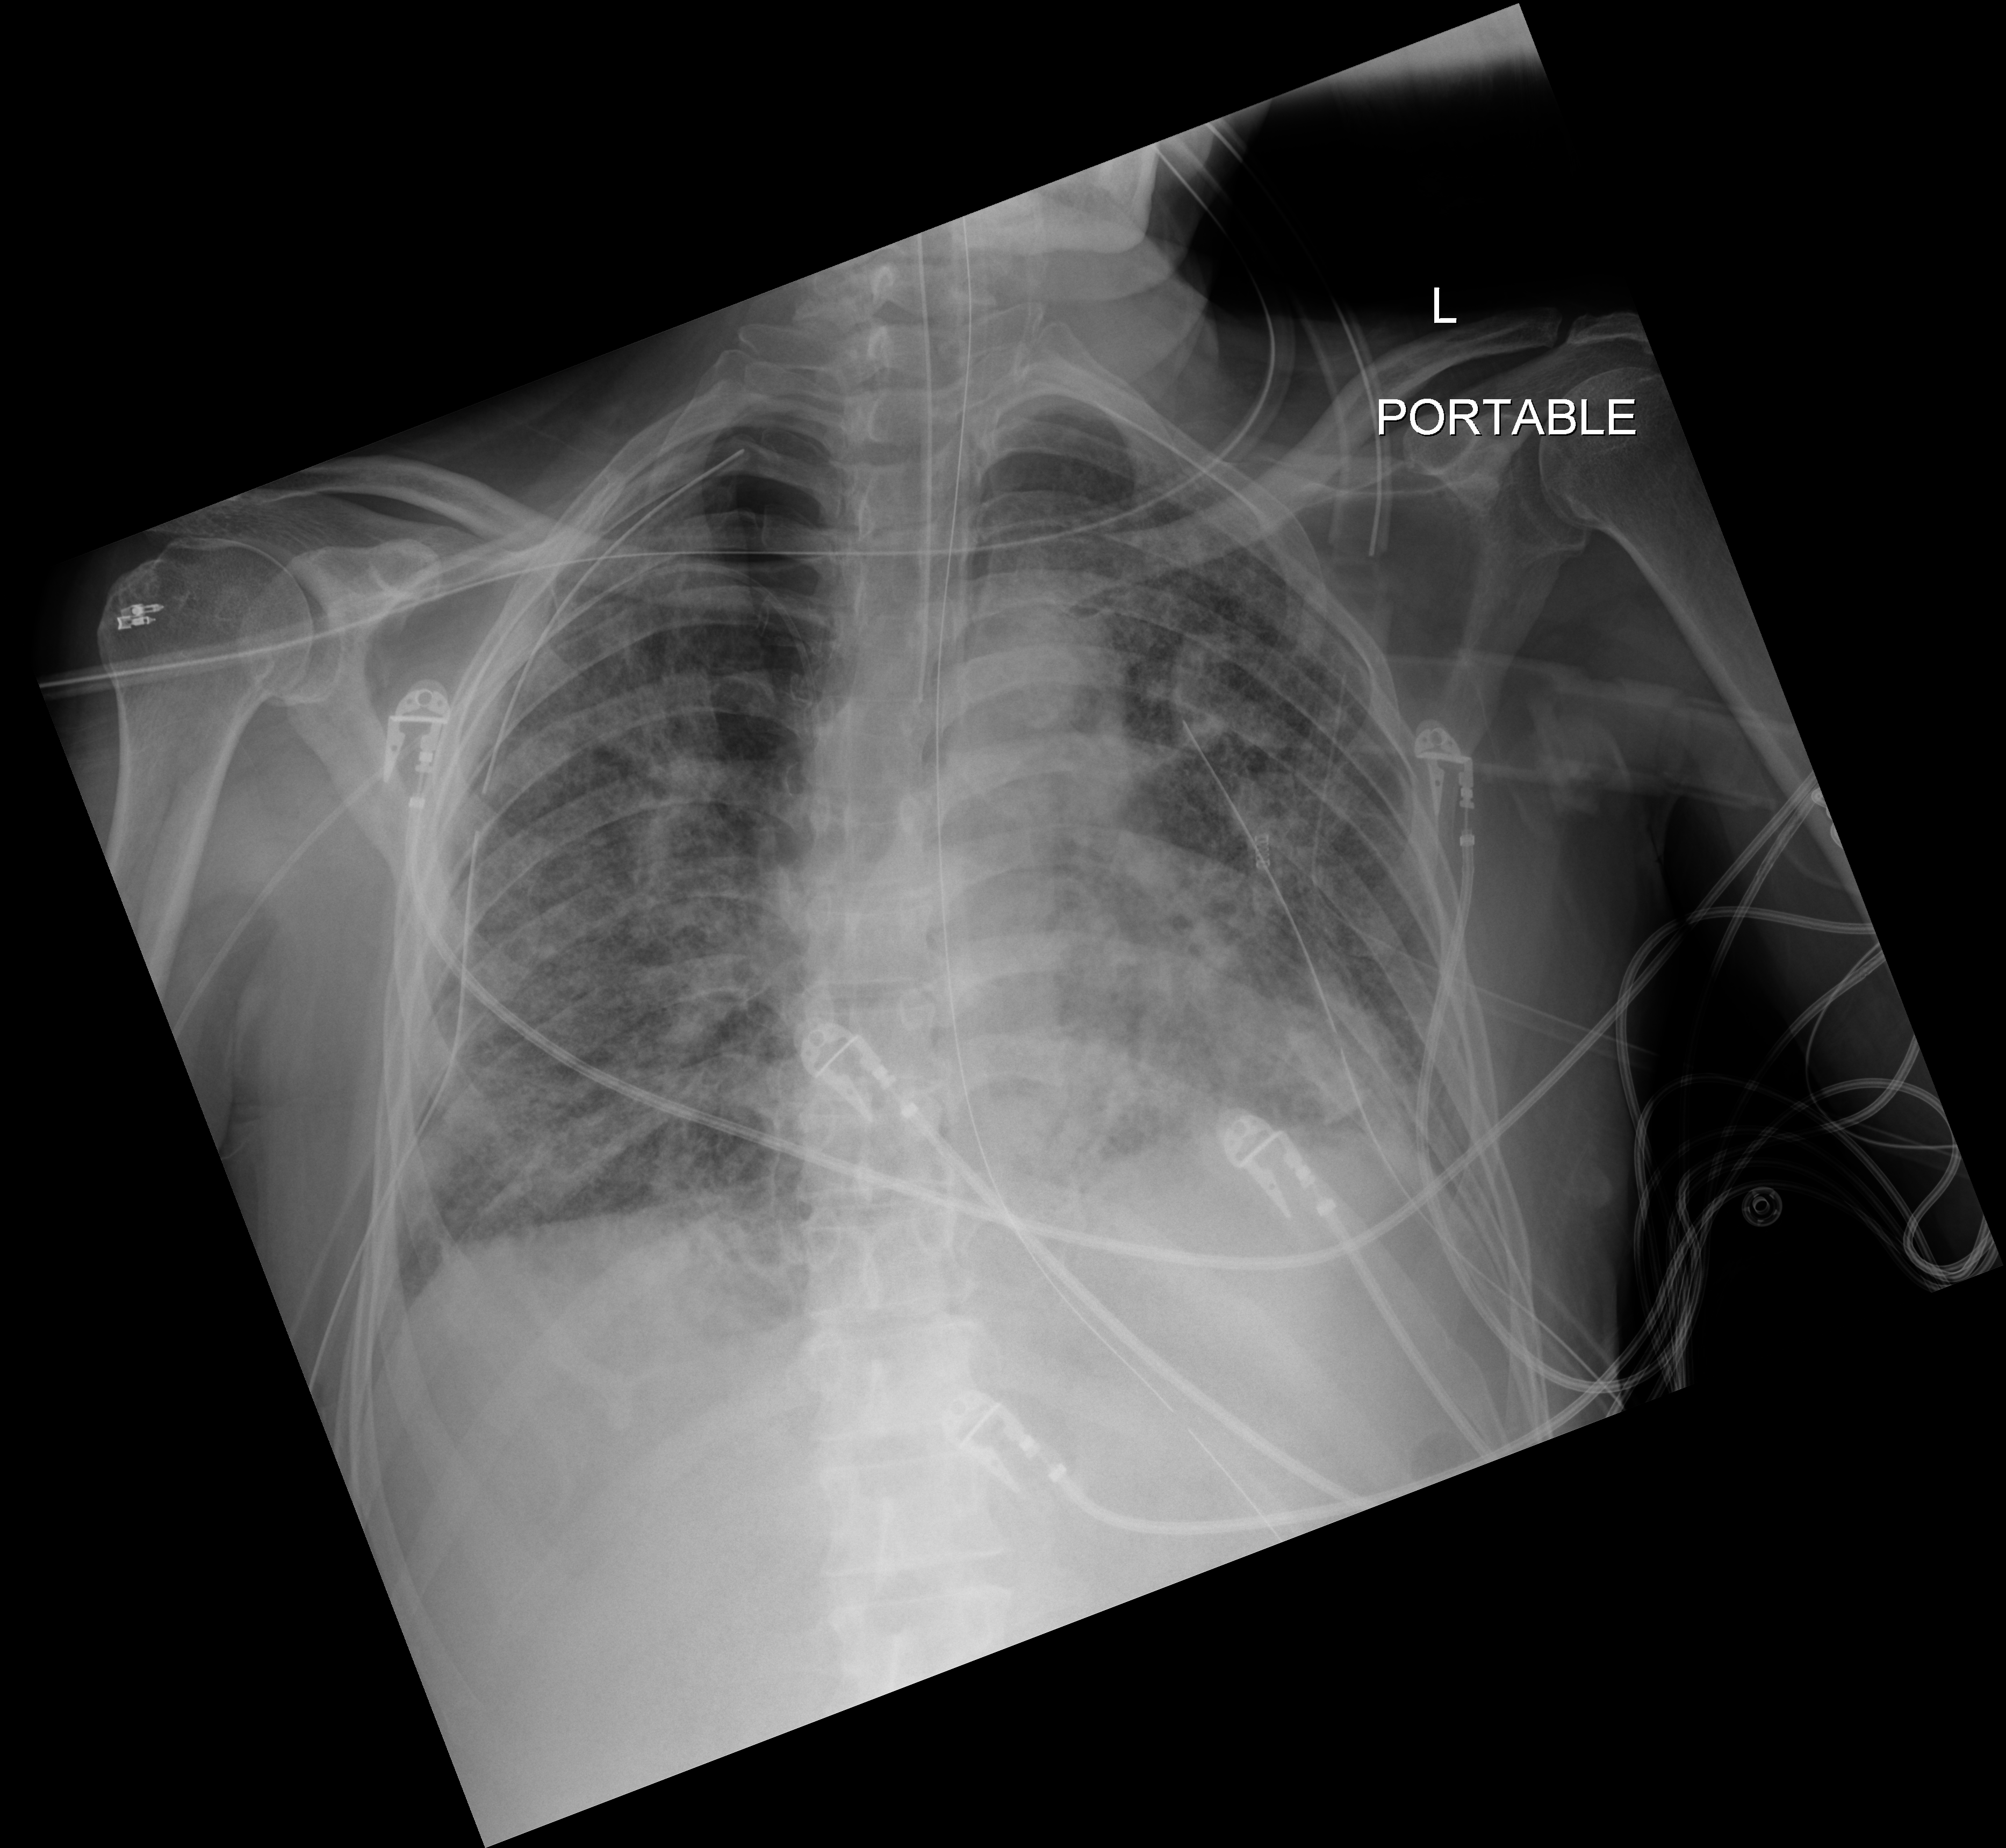
Portable chest radiograph; anteroposterior (AP) projection. Male patient hospitalised with COVID-19, age 60–74 years.
From the hospital-stay record, not from the radiograph (when in the stay this image was taken is not recorded): admitted to intensive care during this hospital stay: yes; mechanically ventilated during this hospital stay: yes.